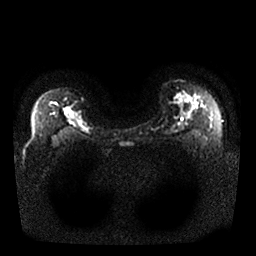
Breast MRI, one axial slice. Slice 19 of 25 in the series (ordered by position). Diffusion-weighted series; image 2 of 4 stored at this slice position (different b-values; order by instance number). 1.5 T. 4 mm slice thickness. 256 × 256 image matrix, field of view 340 × 340 mm. Female patient.
Structures marked on this image (outlined manually by an expert reader):
- tumour on diffusion-weighted imaging: bounding box <64,107,73,121> (left, top, right, bottom; pixels)